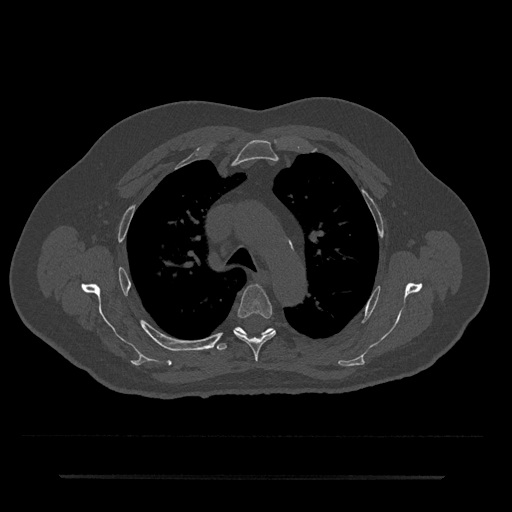
CT including the spine, one axial slice. Slice 517 of 797 in the series (ordered by position). Reconstruction kernel Br40s/3. 120 kVp. Bone window (W 1800 / L 400 HU). 0.5 mm slice thickness. 512 × 512 image matrix, field of view 437 × 437 mm. Patient: male, 69 years. Case-level facts recorded for this patient, not image findings: primary cancer: prostate.
Outlined on this slice (semi-automatically segmented with operator editing):
- T4 vertebra: bounding box [x1, y1, x2, y2] px = [234, 284, 276, 362]
- T5 vertebra: [215, 327, 274, 351]